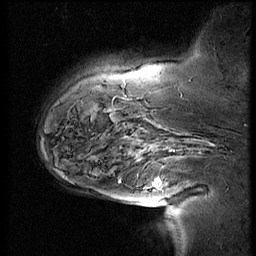
Breast MRI (dynamic contrast-enhanced), one sagittal slice; slice 15 of 60 in the series (ordered by position); 4 images stored at this slice position (order not interpretable as contrast timing); 1.5 T; TE 4.2 ms, TR 9 ms; 2.5 mm slice thickness; 256 × 256 image matrix, field of view 180 × 180 mm. Female patient, age 56 years. From the clinical record (not read from this slice): setting: breast cancer imaged before/during neoadjuvant chemotherapy; receptor status: HER2-positive.
Outlined on this slice (semi-automatic segmentation, software-assisted and operator-edited):
- analysis volume of interest (the breast-tissue region the enhancement analysis was run in; not a lesion): bounding box (x1, y1, x2, y2) in pixels: (110, 138, 192, 201)
- tumour enhancement mask (voxels above the 140 % enhancement threshold inside the analysis volume of interest): (119, 179, 160, 186)